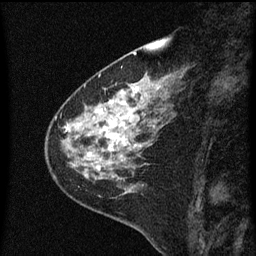
Breast MRI (dynamic contrast-enhanced), one sagittal slice; position 19 of 60 along the scan axis; dynamic contrast-enhanced series, image 2 of 3 at this slice position (ordered by acquisition); 1.5 T; TE 4.2 ms, TR 8 ms; 2 mm slice thickness; 256 × 256 image matrix, field of view 180 × 180 mm. Female patient, age 60 years.
Outlined on this slice (semi-automatically segmented with operator editing):
- analysis volume of interest (the breast-tissue region the enhancement analysis was run in; not a lesion): bounding box (x1, y1, x2, y2) in pixels: (48, 82, 159, 181)
- tumour enhancement mask (voxels above the 70 % enhancement threshold inside the analysis volume of interest): (67, 86, 144, 171)